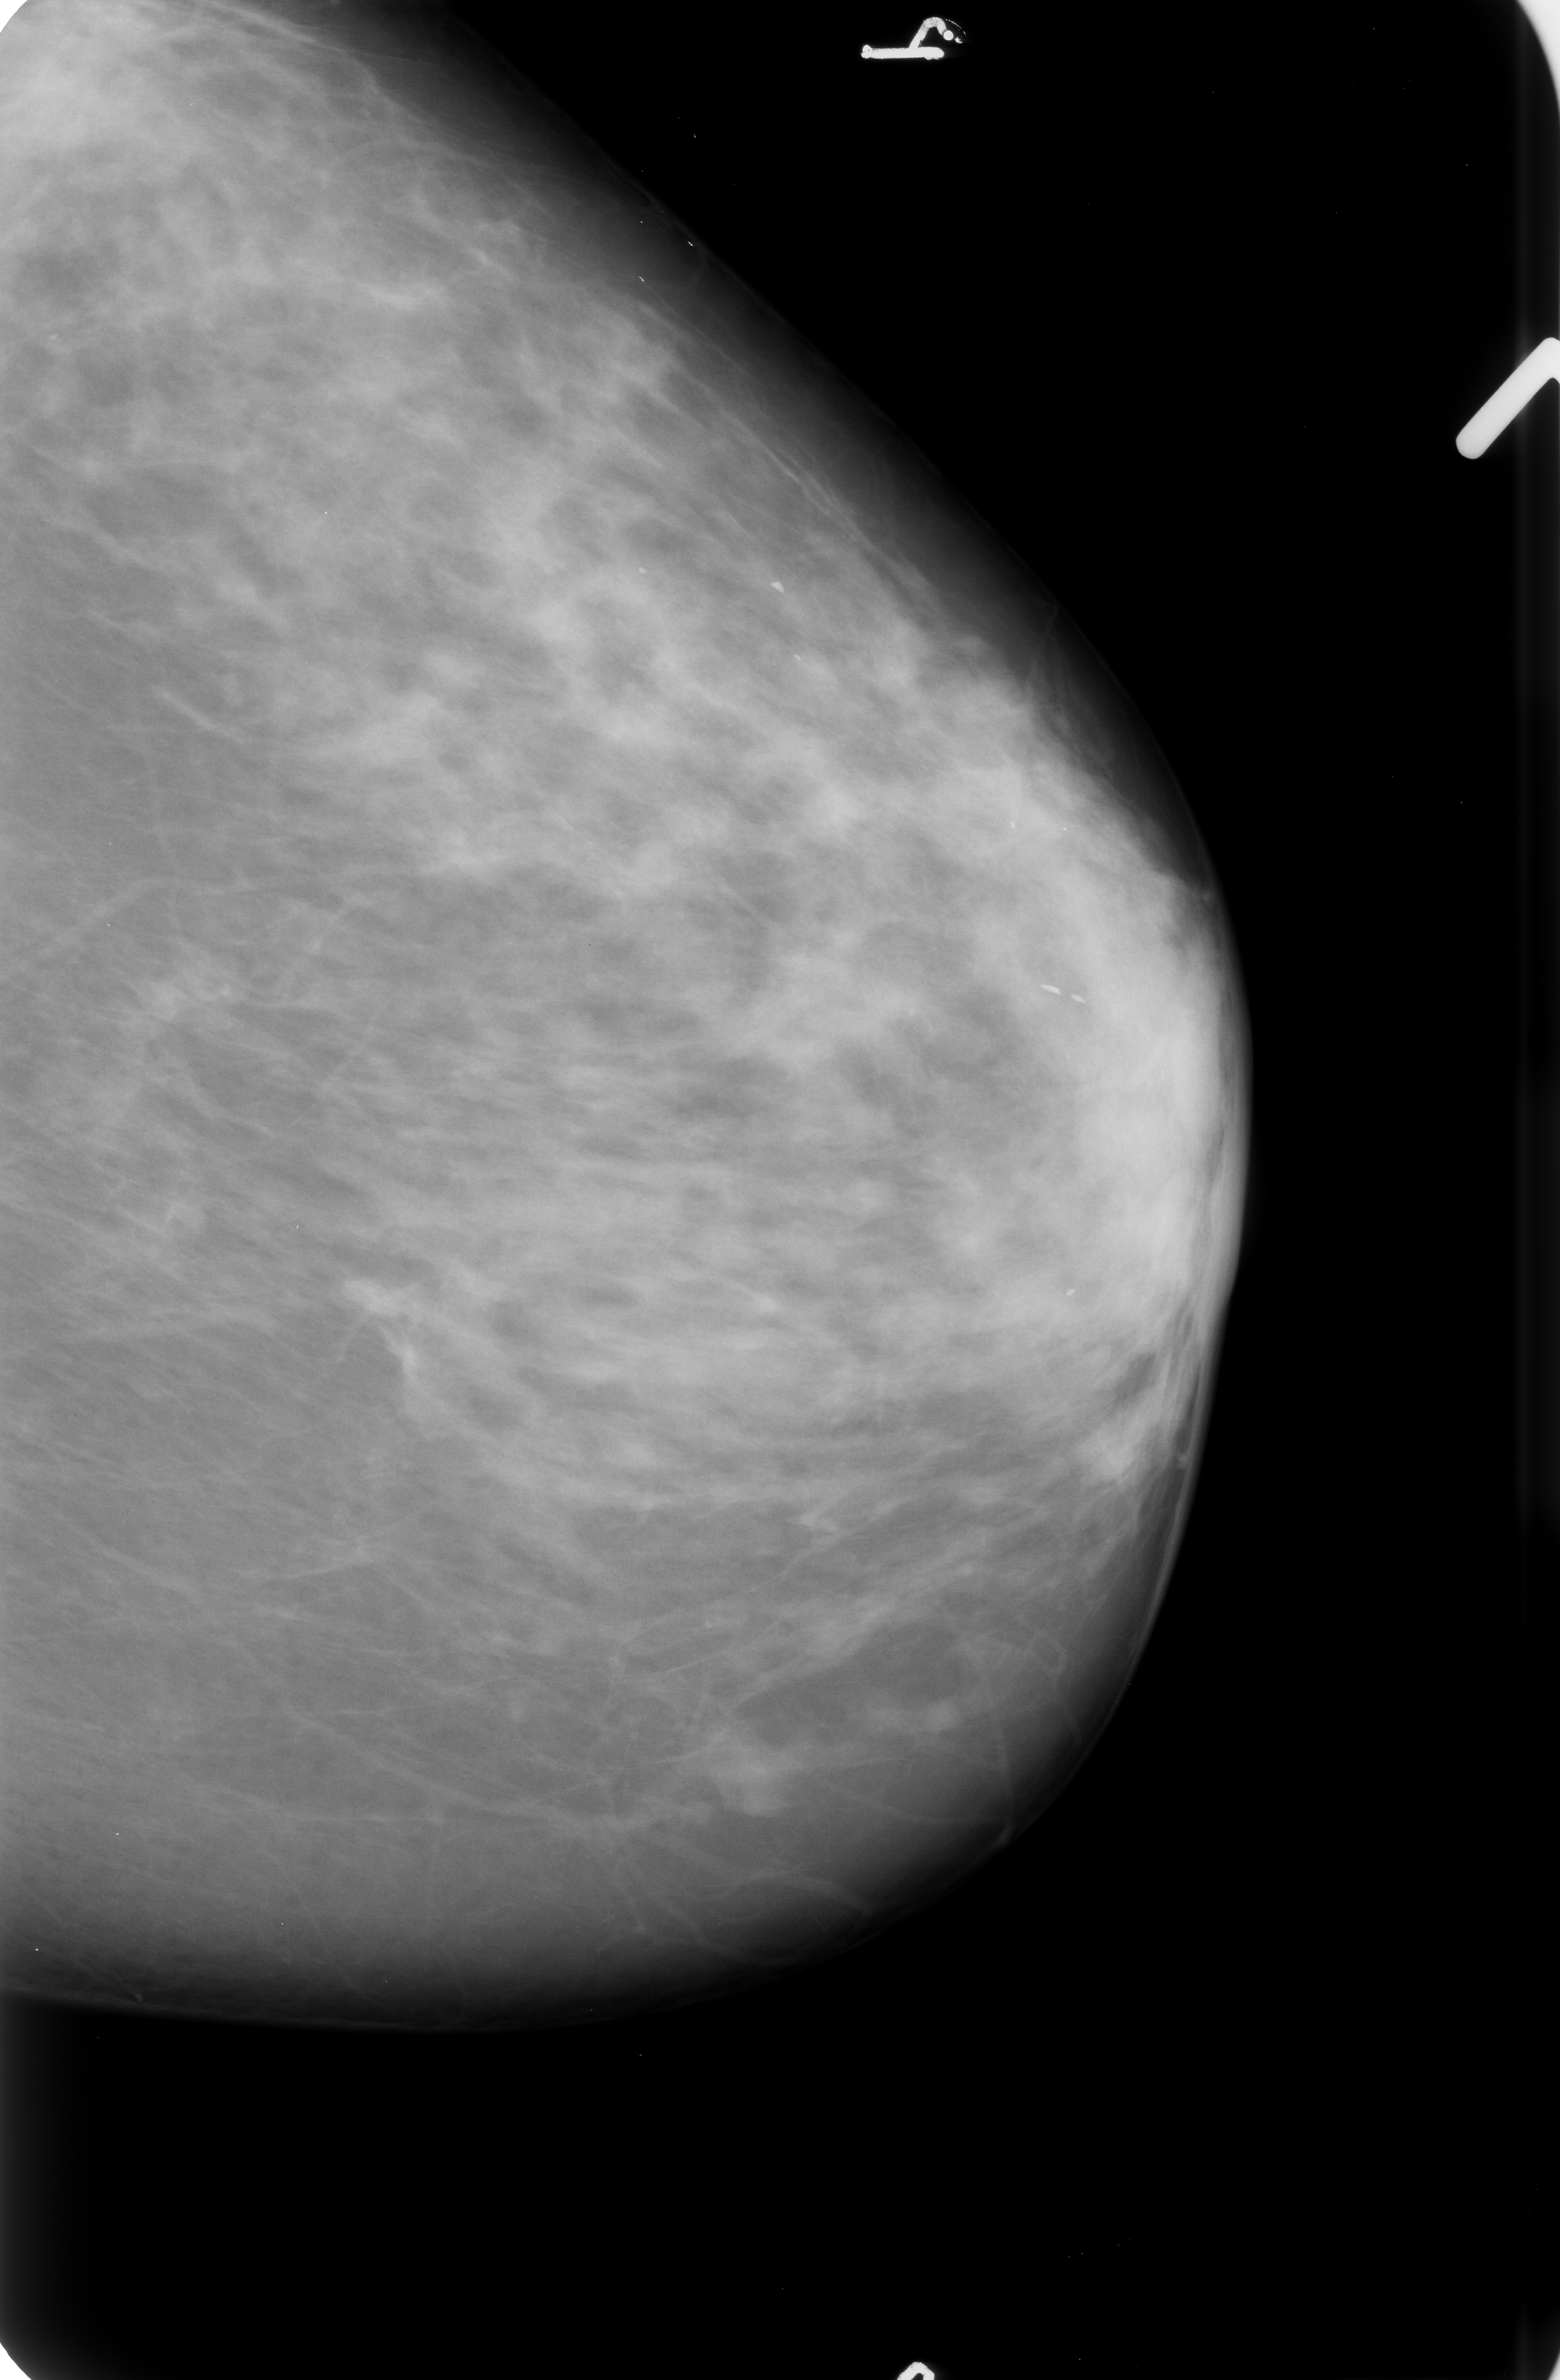
Scanned film-screen mammogram; left breast; CC view; BI-RADS breast density category 3 (scale 1–4); 1560 × 2380 image matrix.
Expert-marked regions of interest on this film, with their recorded descriptors:
- Finding 1 of 3: calcifications, morphology vascular / coarse; BI-RADS assessment category 2; subtlety rating 3 on a 1 (subtle) to 5 (obvious) scale; benign; no additional work-up was recommended (outcome (as recorded, no biopsy): benign without callback): bounding box [x1, y1, x2, y2] px = [751, 560, 809, 618]
- Finding 2 of 3: calcifications, morphology vascular / coarse; BI-RADS assessment category 2; benign; no additional work-up was recommended (outcome (as recorded, no biopsy): benign without callback): [771, 637, 830, 700]
- Finding 3 of 3: calcifications, morphology vascular / coarse; BI-RADS assessment category 2; subtlety rating 3 on a 1 (subtle) to 5 (obvious) scale; benign; no additional work-up was recommended (outcome (as recorded, no biopsy): benign without callback): [1019, 962, 1110, 1029]